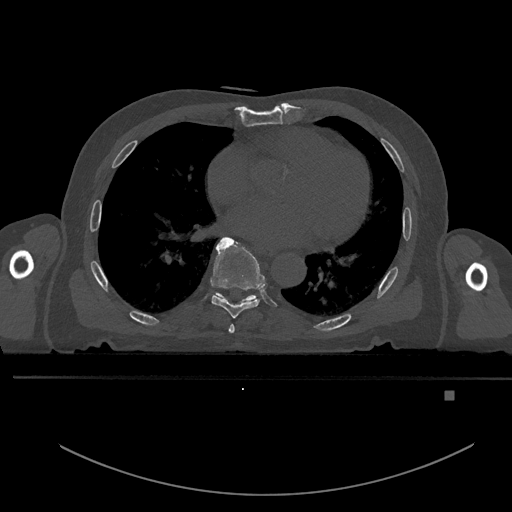
CT including the spine, one axial slice; slice 244 of 969 in the series (ordered by position); bone window (W 1800 / L 400 HU); 0.5 mm slice thickness; 512 × 512 image matrix, field of view 456 × 456 mm. Male patient, age 82 years. From the clinical record (not read from this slice): primary cancer: prostate.
Outlined on this slice (semi-automatic segmentation, software-assisted and operator-edited):
- T6 vertebra: bounding box [x1, y1, x2, y2] px = [229, 324, 235, 333]
- T7 vertebra: [211, 237, 265, 318]
- T8 vertebra: [213, 293, 258, 304]